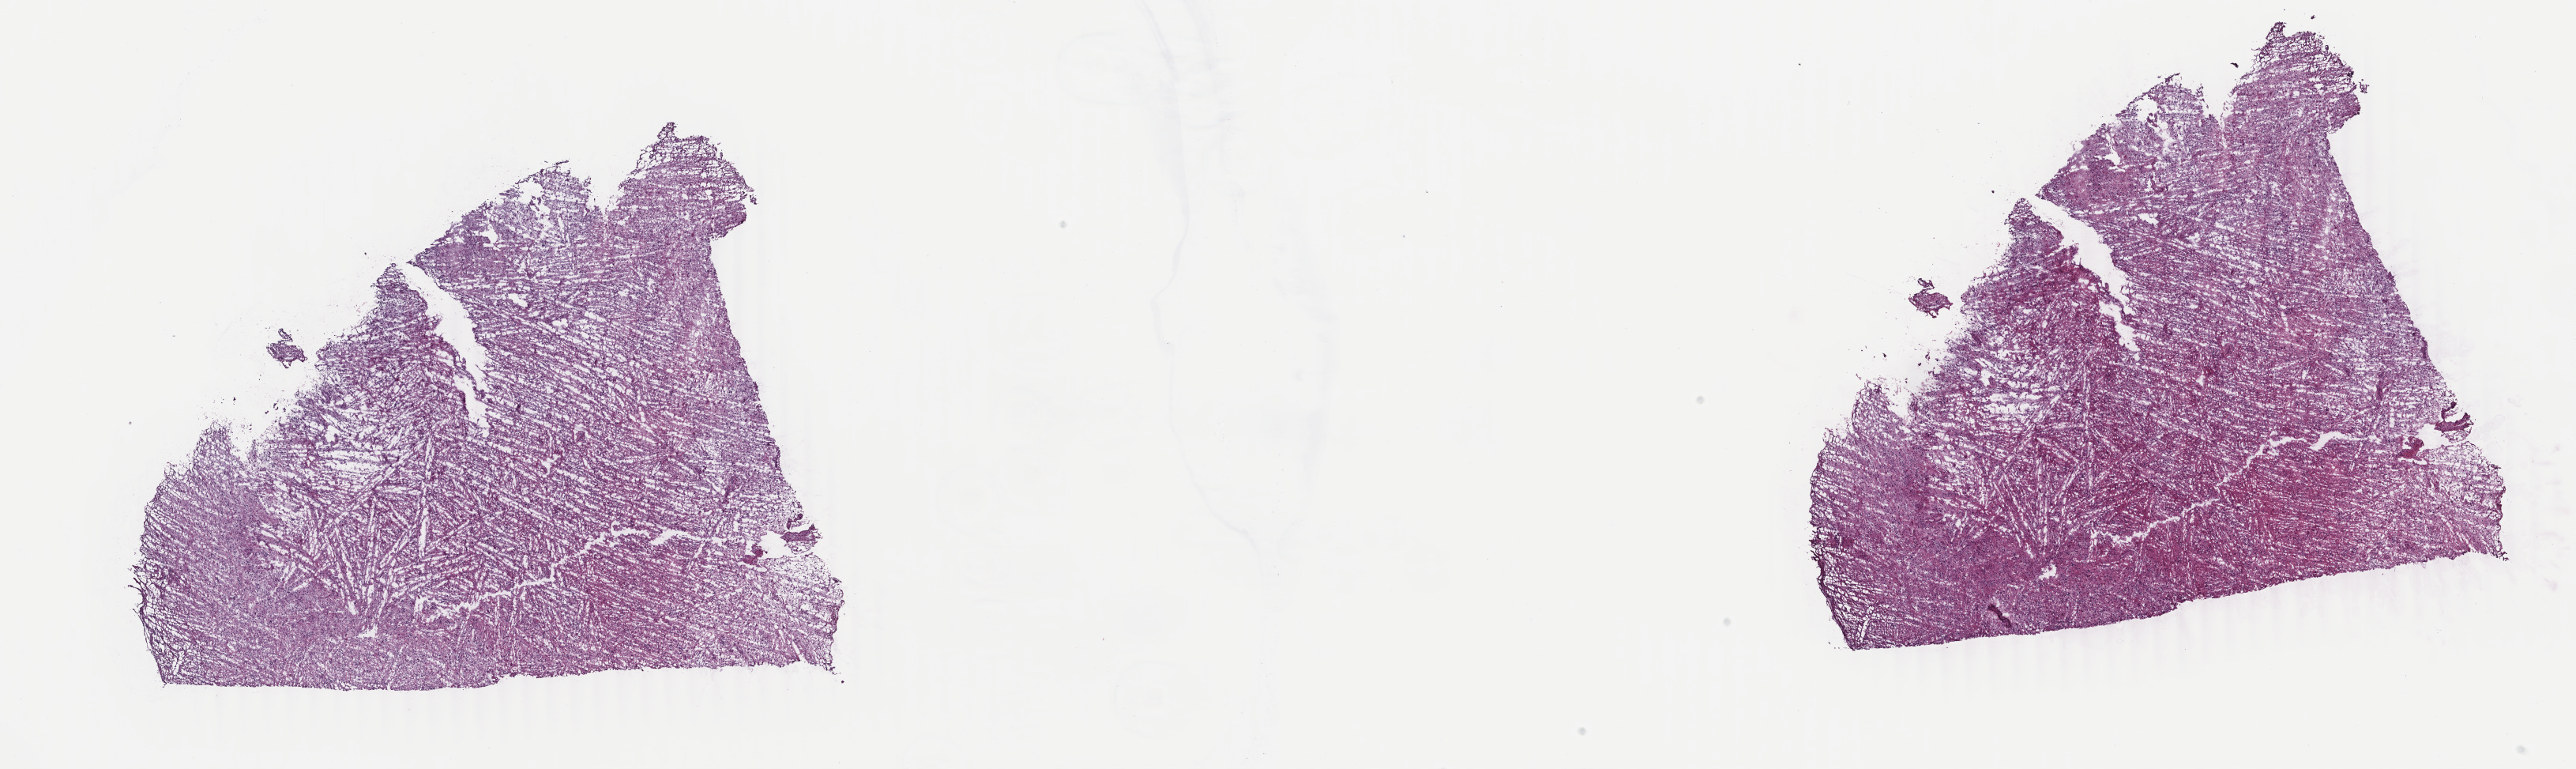
Digitized H&E-stained tissue section (whole slide) — shown as a low-resolution overview of the whole scanned area (about 25.9 x 7.7 mm, from a 40x scan); frozen section; brain, primary tumour sample. Male patient; age at initial diagnosis 35 years. Histologic grade: G3 (poorly differentiated). Slide review estimates, as recorded: tumour cells 50%, tumour nuclei 80%, normal cells 5%, stromal cells 45%, necrosis 0%. Infiltration values recorded for this section: lymphocyte infiltration 0%, monocyte infiltration 0%, neutrophil infiltration 0%.
Histologic diagnosis: Astrocytoma, anaplastic (cerebrum). Laterality: right.